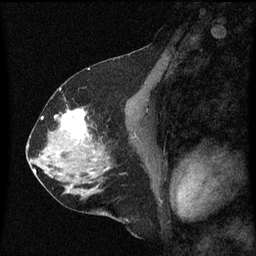
Breast MRI (dynamic contrast-enhanced), one sagittal slice. Slice 31 of 60 in the series (ordered by position). Dynamic contrast-enhanced series, image 2 of 3 at this slice position (ordered by acquisition). 1.5 T. TE 4.2 ms, TR 8 ms. 256 × 256 image matrix. Female patient, age 58 years.
Structures marked on this image (semi-automatically segmented with operator editing):
- analysis volume of interest (the breast-tissue region the enhancement analysis was run in; not a lesion): bounding box <56,108,99,149> (left, top, right, bottom; pixels)
- tumour enhancement mask (voxels above the 70 % enhancement threshold inside the analysis volume of interest): <62,110,87,139>